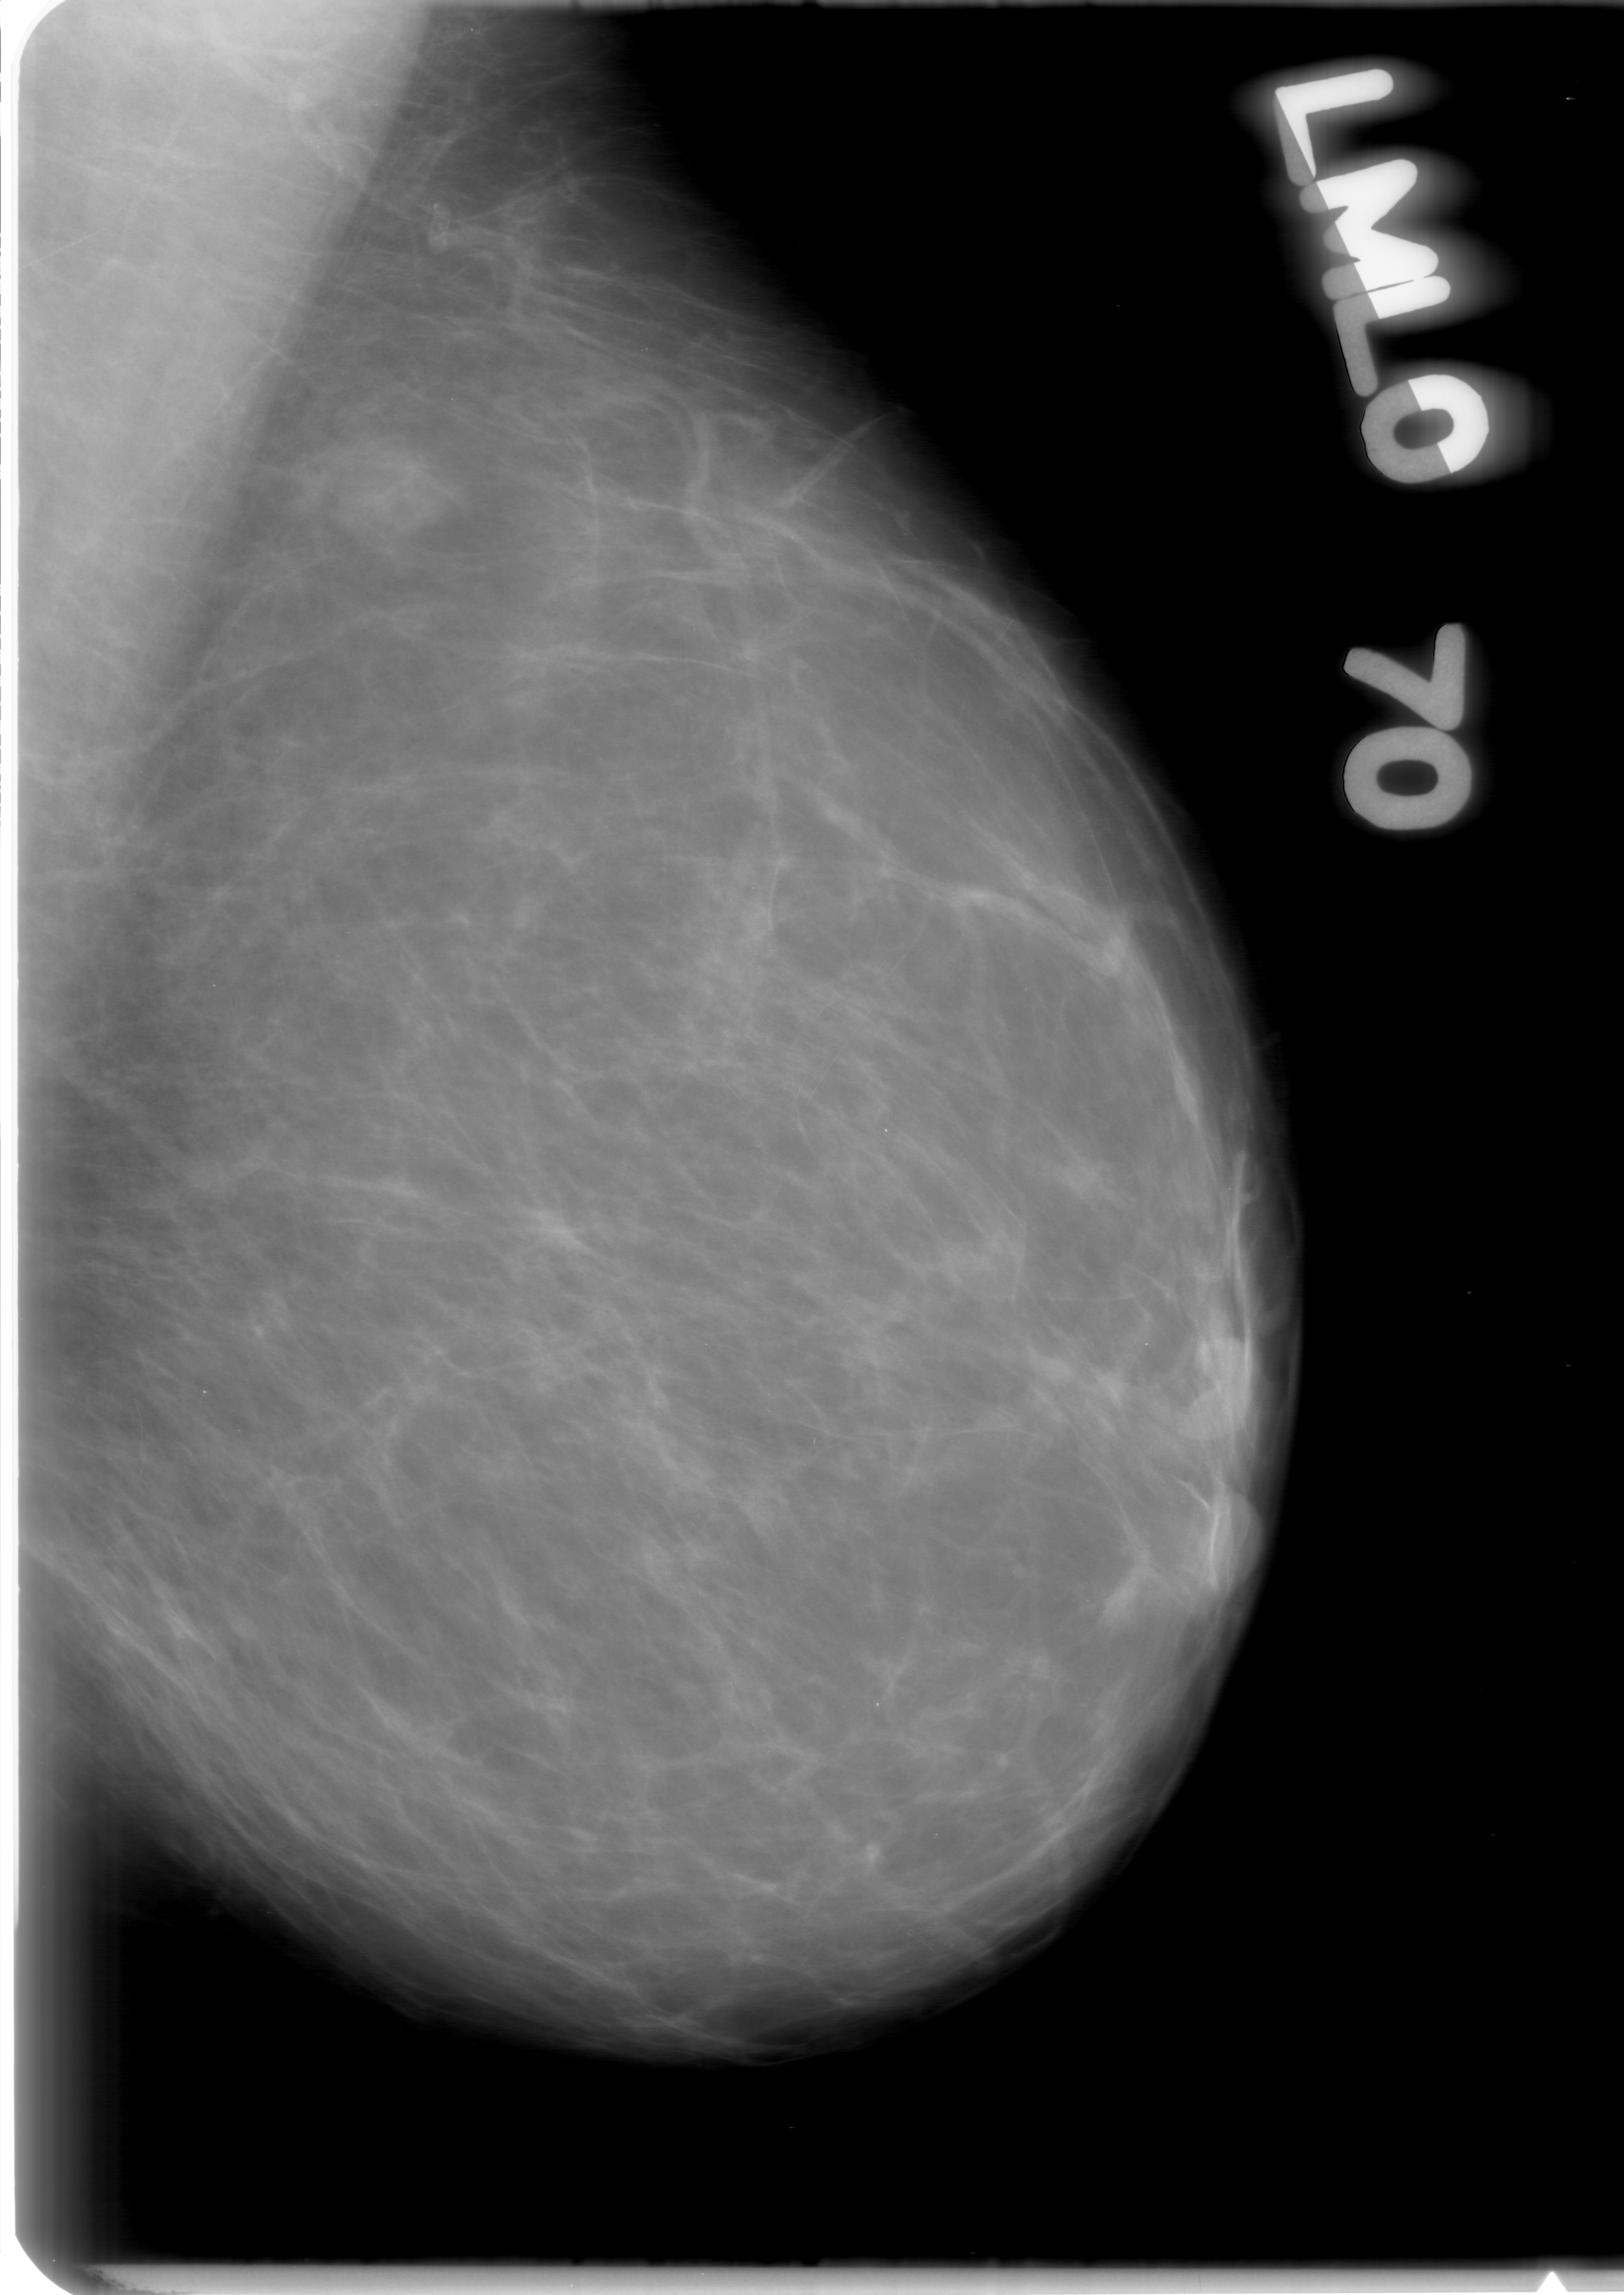
Digitized screen-film mammogram, left breast, MLO view.
- Marked abnormality: mass, shape irregular, margins obscured; BI-RADS assessment category 0 (incomplete: needs additional imaging); pathology (as recorded): benign.